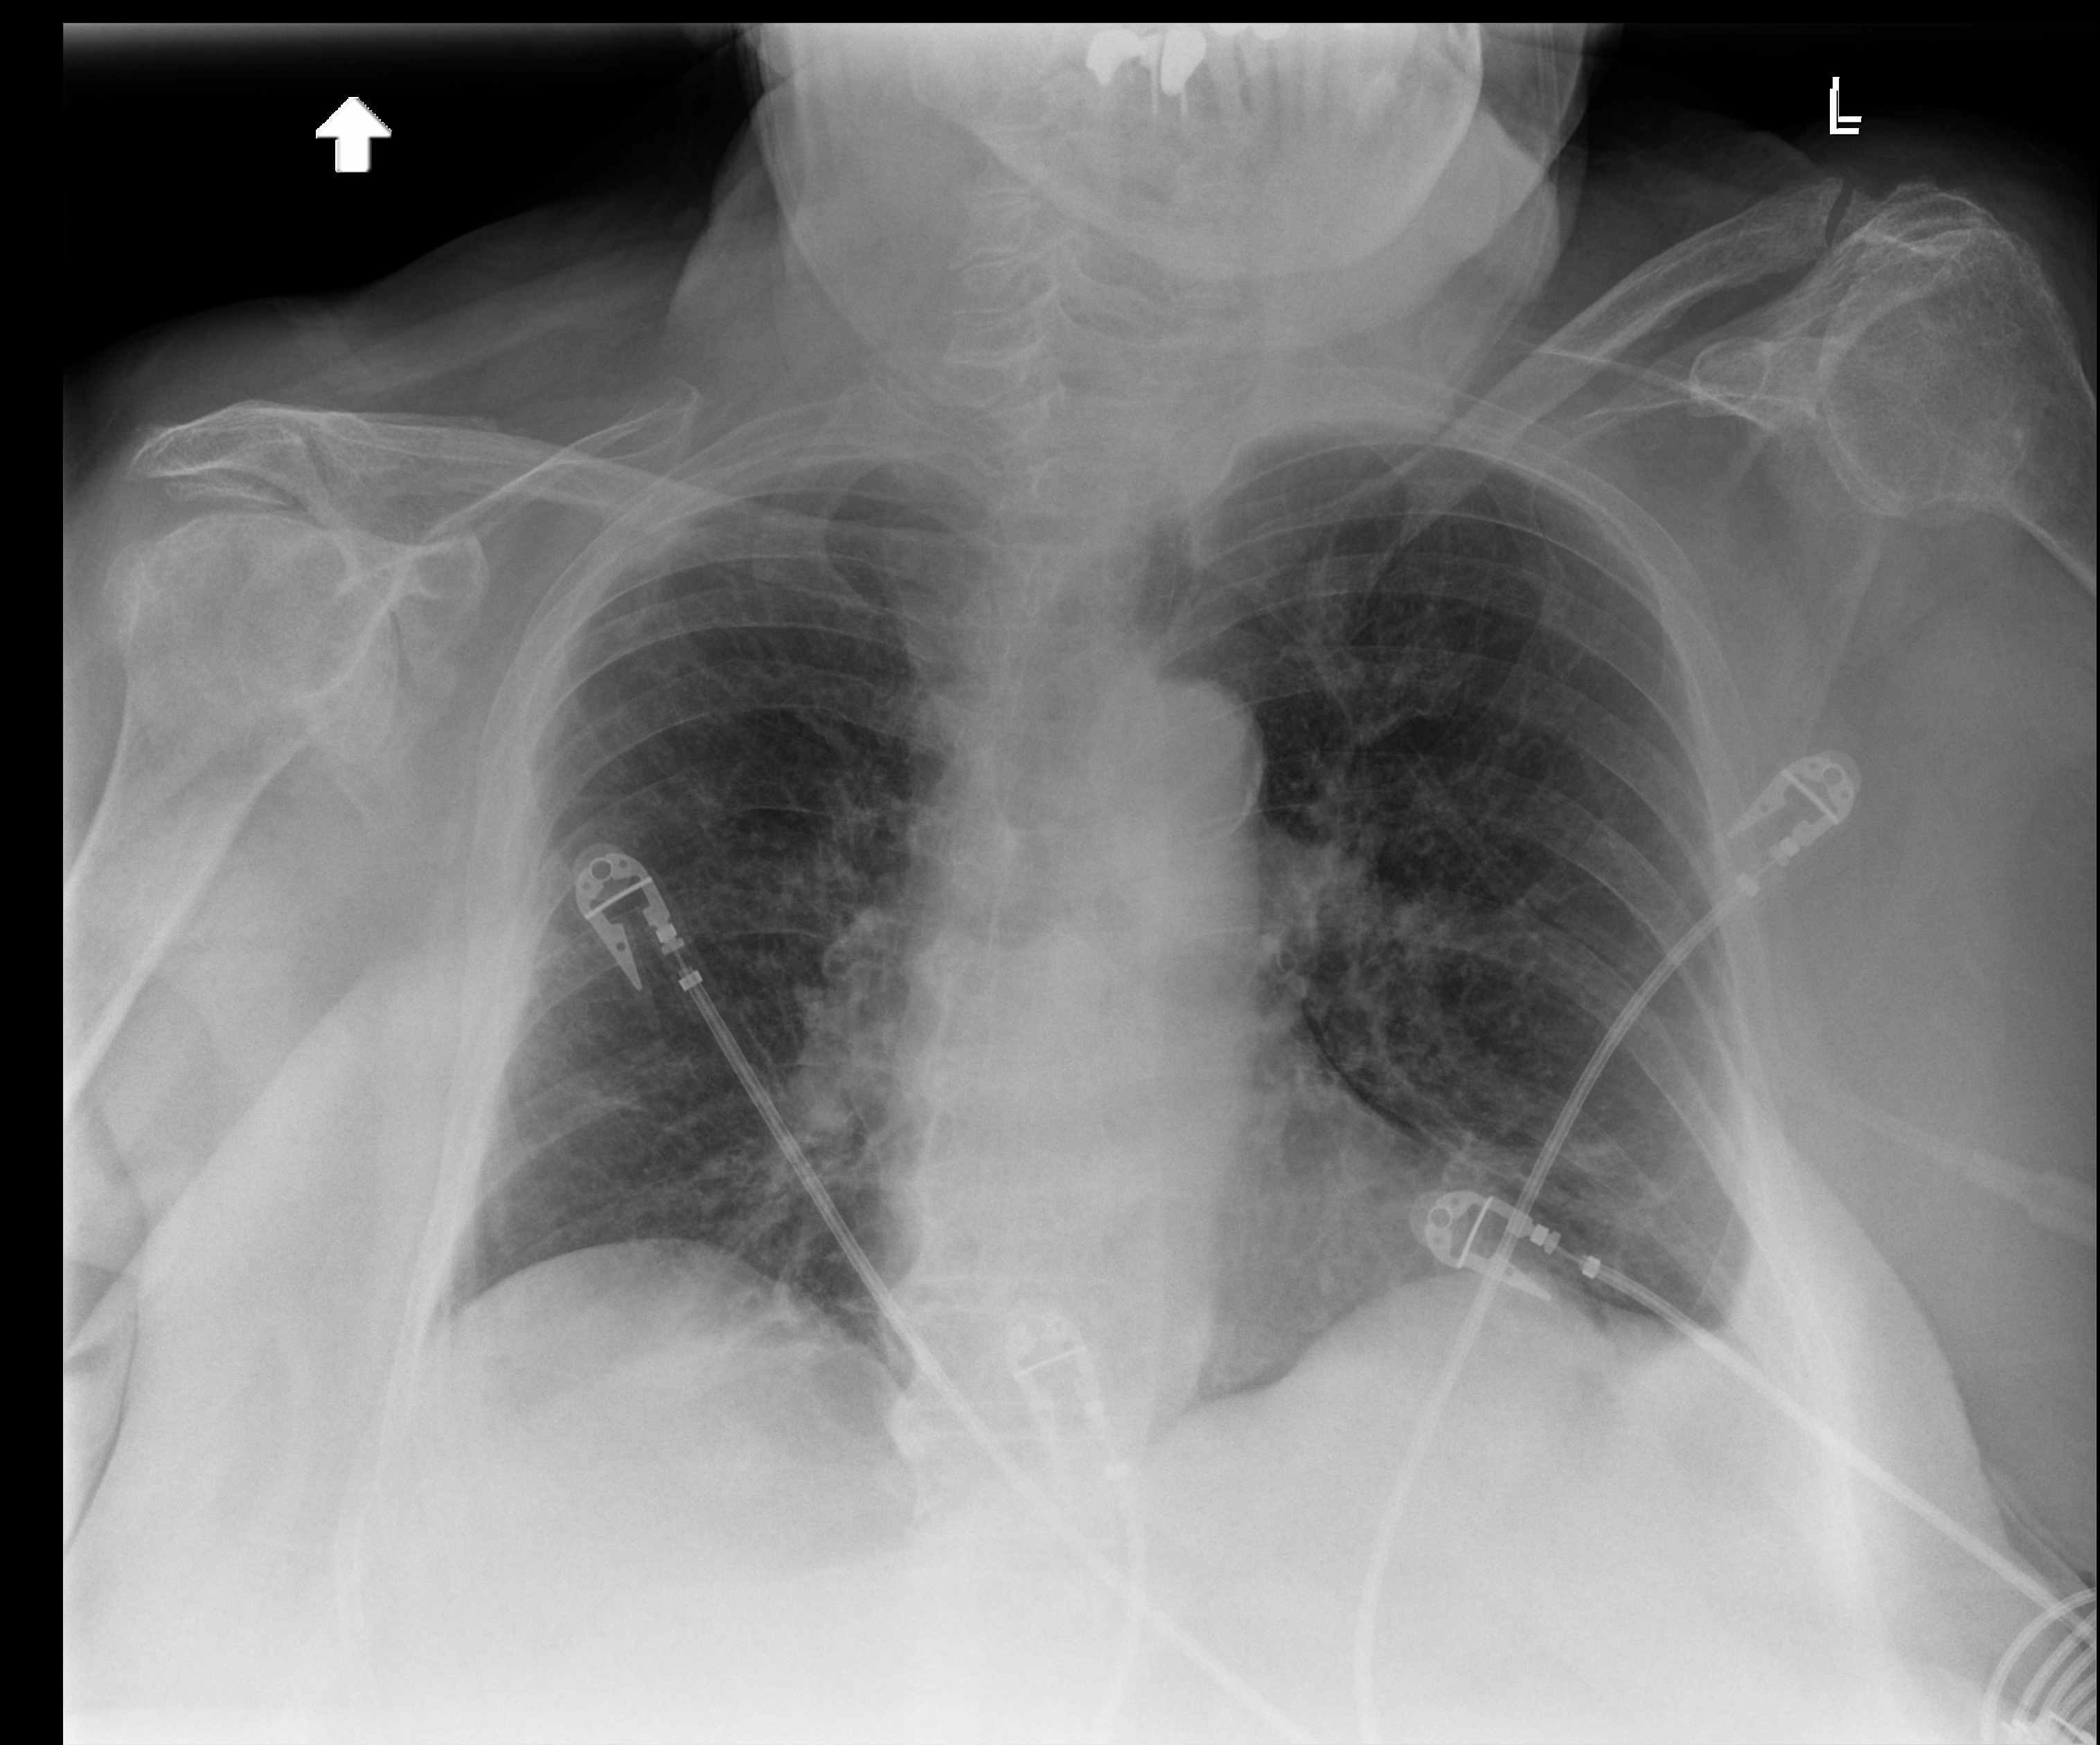
Chest X-ray (portable), anteroposterior (AP) projection. Female patient hospitalised with COVID-19, age 75–90 years.
From the hospital-stay record, not from the radiograph (when in the stay this image was taken is not recorded):
- length of hospital stay: 2 days